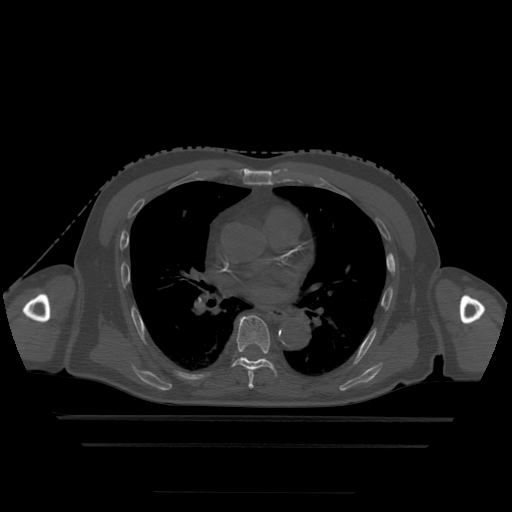
CT including the spine, one axial slice; position 301 of 522 along the scan axis; bone window (W 1800 / L 400 HU); 1.25 mm slice thickness; 512 × 512 image matrix, field of view 436 × 436 mm. Patient age 68 years. From the clinical record (not read from this slice): primary cancer: urothelial.
Structures marked on this image (semi-automatically segmented with operator editing):
- T5 vertebra: bounding box [x1, y1, x2, y2] px = [249, 384, 253, 387]
- T6 vertebra: [248, 369, 255, 389]
- T7 vertebra: [233, 316, 274, 371]